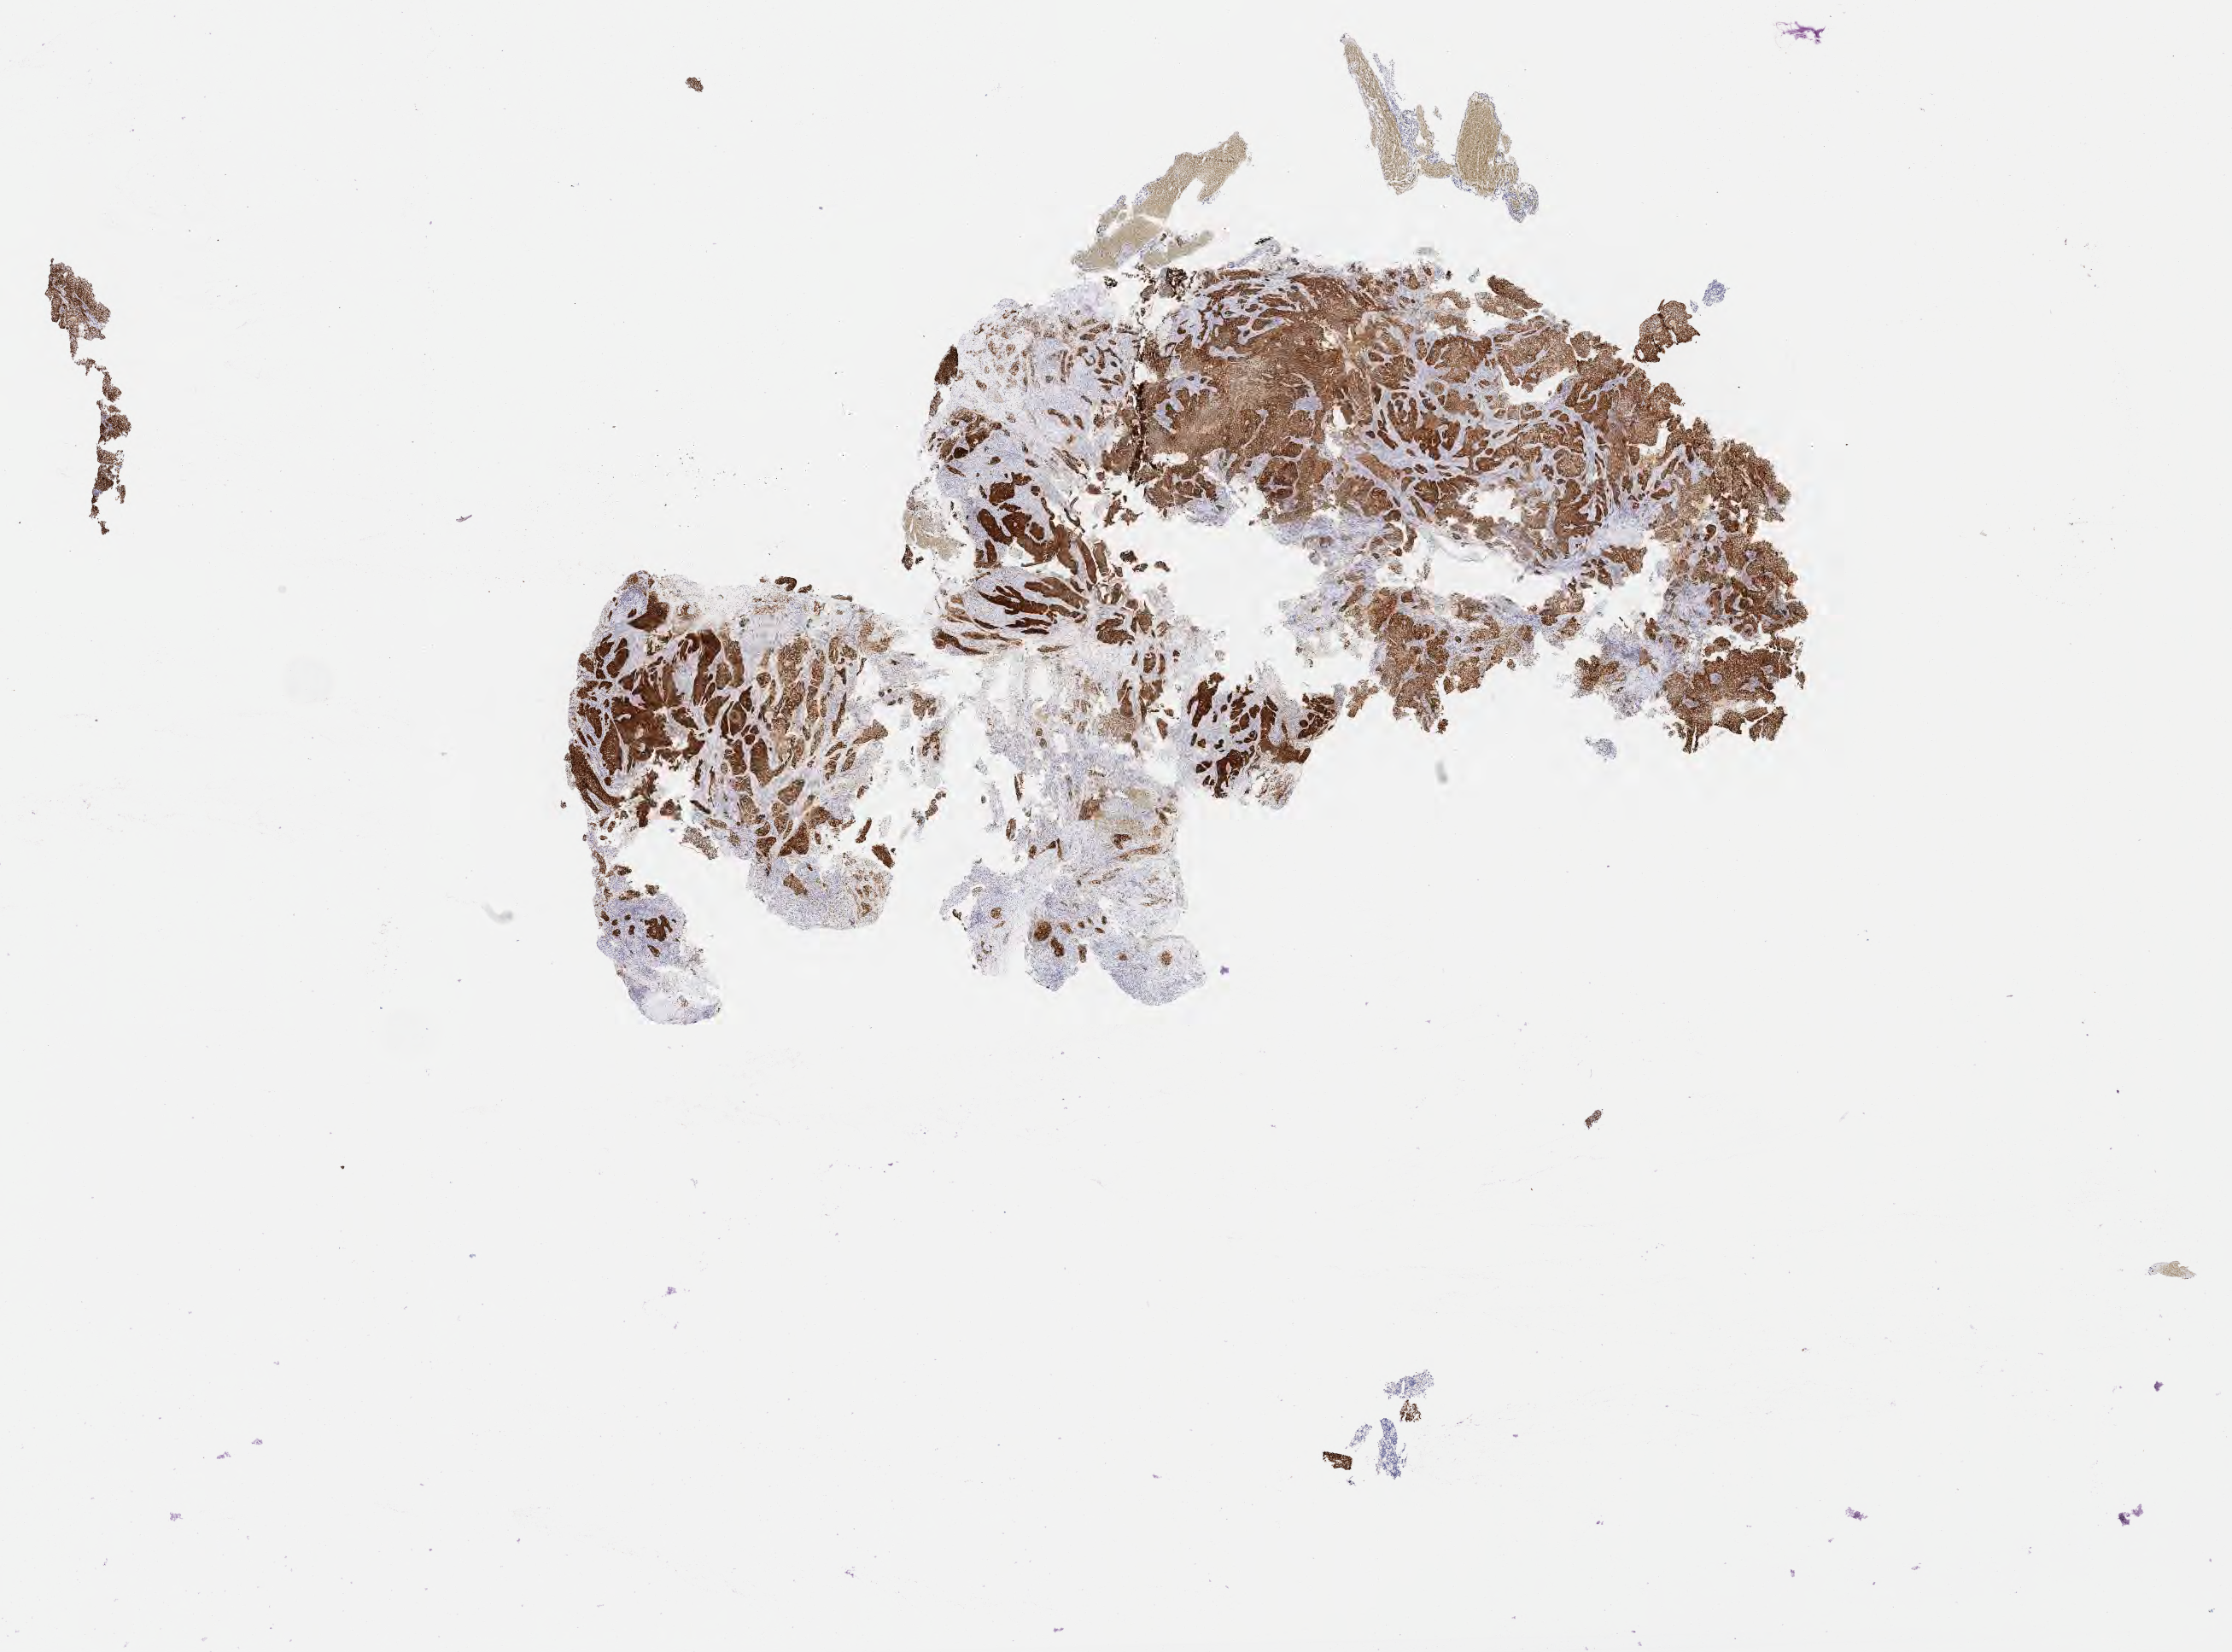
IHC for p16 (p16INK4a), whole-slide image, a low-resolution overview of the entire scanned area, about 21.1 x 15.6 mm, specimen: tumor tissue, anatomic site: cervix. Patient: female, 46 years old.
* histologic diagnosis: Squamous cell carcinoma, large cell, nonkeratinizing, NOS